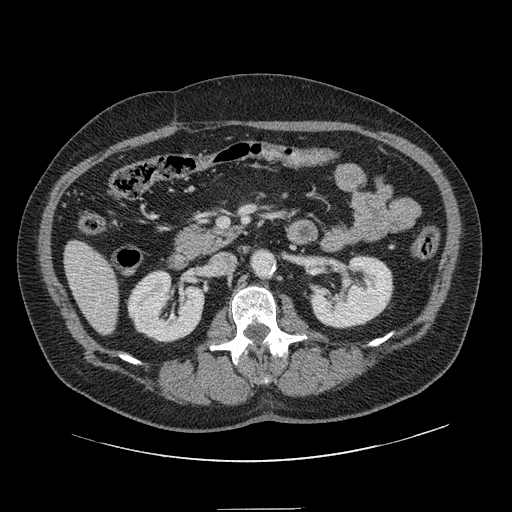
Contrast-enhanced abdominal CT, one axial slice; slice 47 of 154 in the series (ordered by position); intravenous contrast given; soft-tissue window (W 400 / L 40 HU); 512 × 512 image matrix. Male patient, age 61 years. Case-level facts recorded for this patient, not image findings: diagnosis: colorectal cancer liver metastases, imaged before liver resection; multiple liver metastases: yes; largest metastasis: 2.6 cm; disease in both lobes: yes.
Outlined on this slice (expert manual segmentation):
- hepatic veins: bounding box (x1, y1, x2, y2) in pixels: (81, 268, 100, 303)
- liver: (66, 242, 119, 334)
- planned liver remnant (the part of the liver to remain after resection): (66, 242, 119, 334)